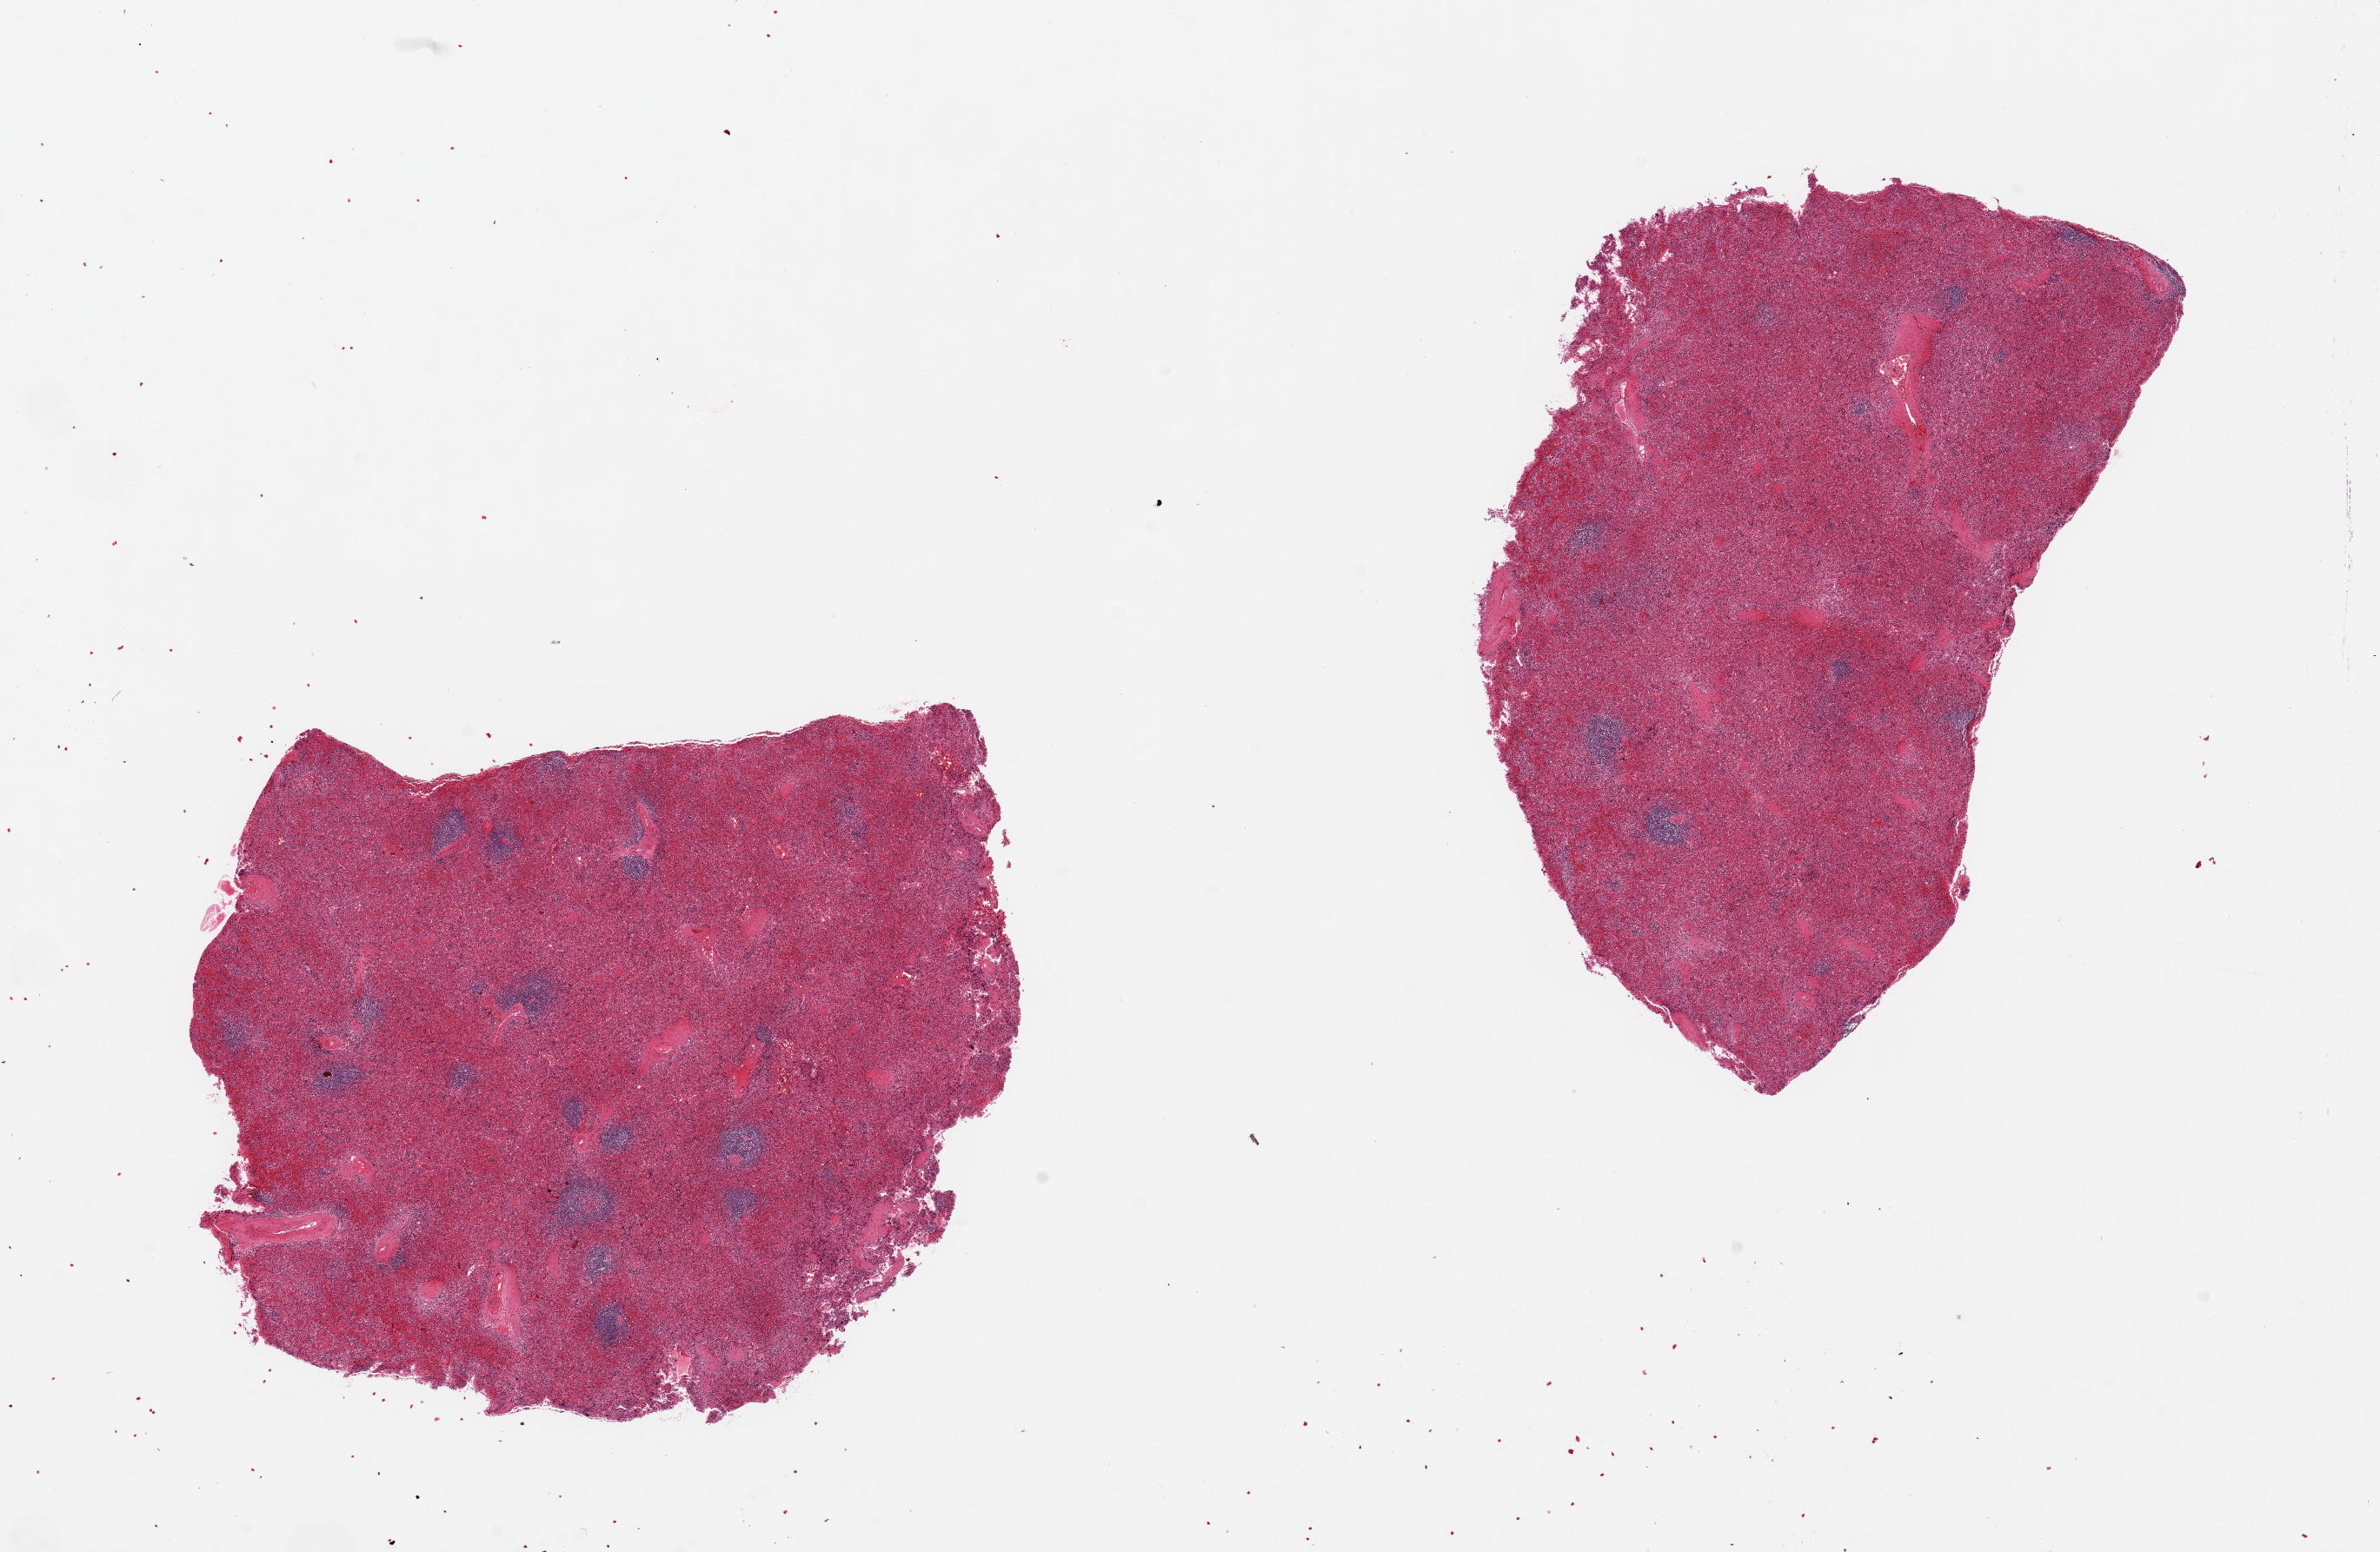
Digitized hematoxylin and eosin (H&E)-stained section, low-resolution overview of the scanned area, about 21.7 x 14.1 mm; PAXgene-fixed, paraffin-embedded tissue; sampled site (target tissue): spleen; donor tissue sample. Donor: male.
Pathologist's review note for this sample: 2 pieces, 7x7 & 8x5mm; moderate congestion.